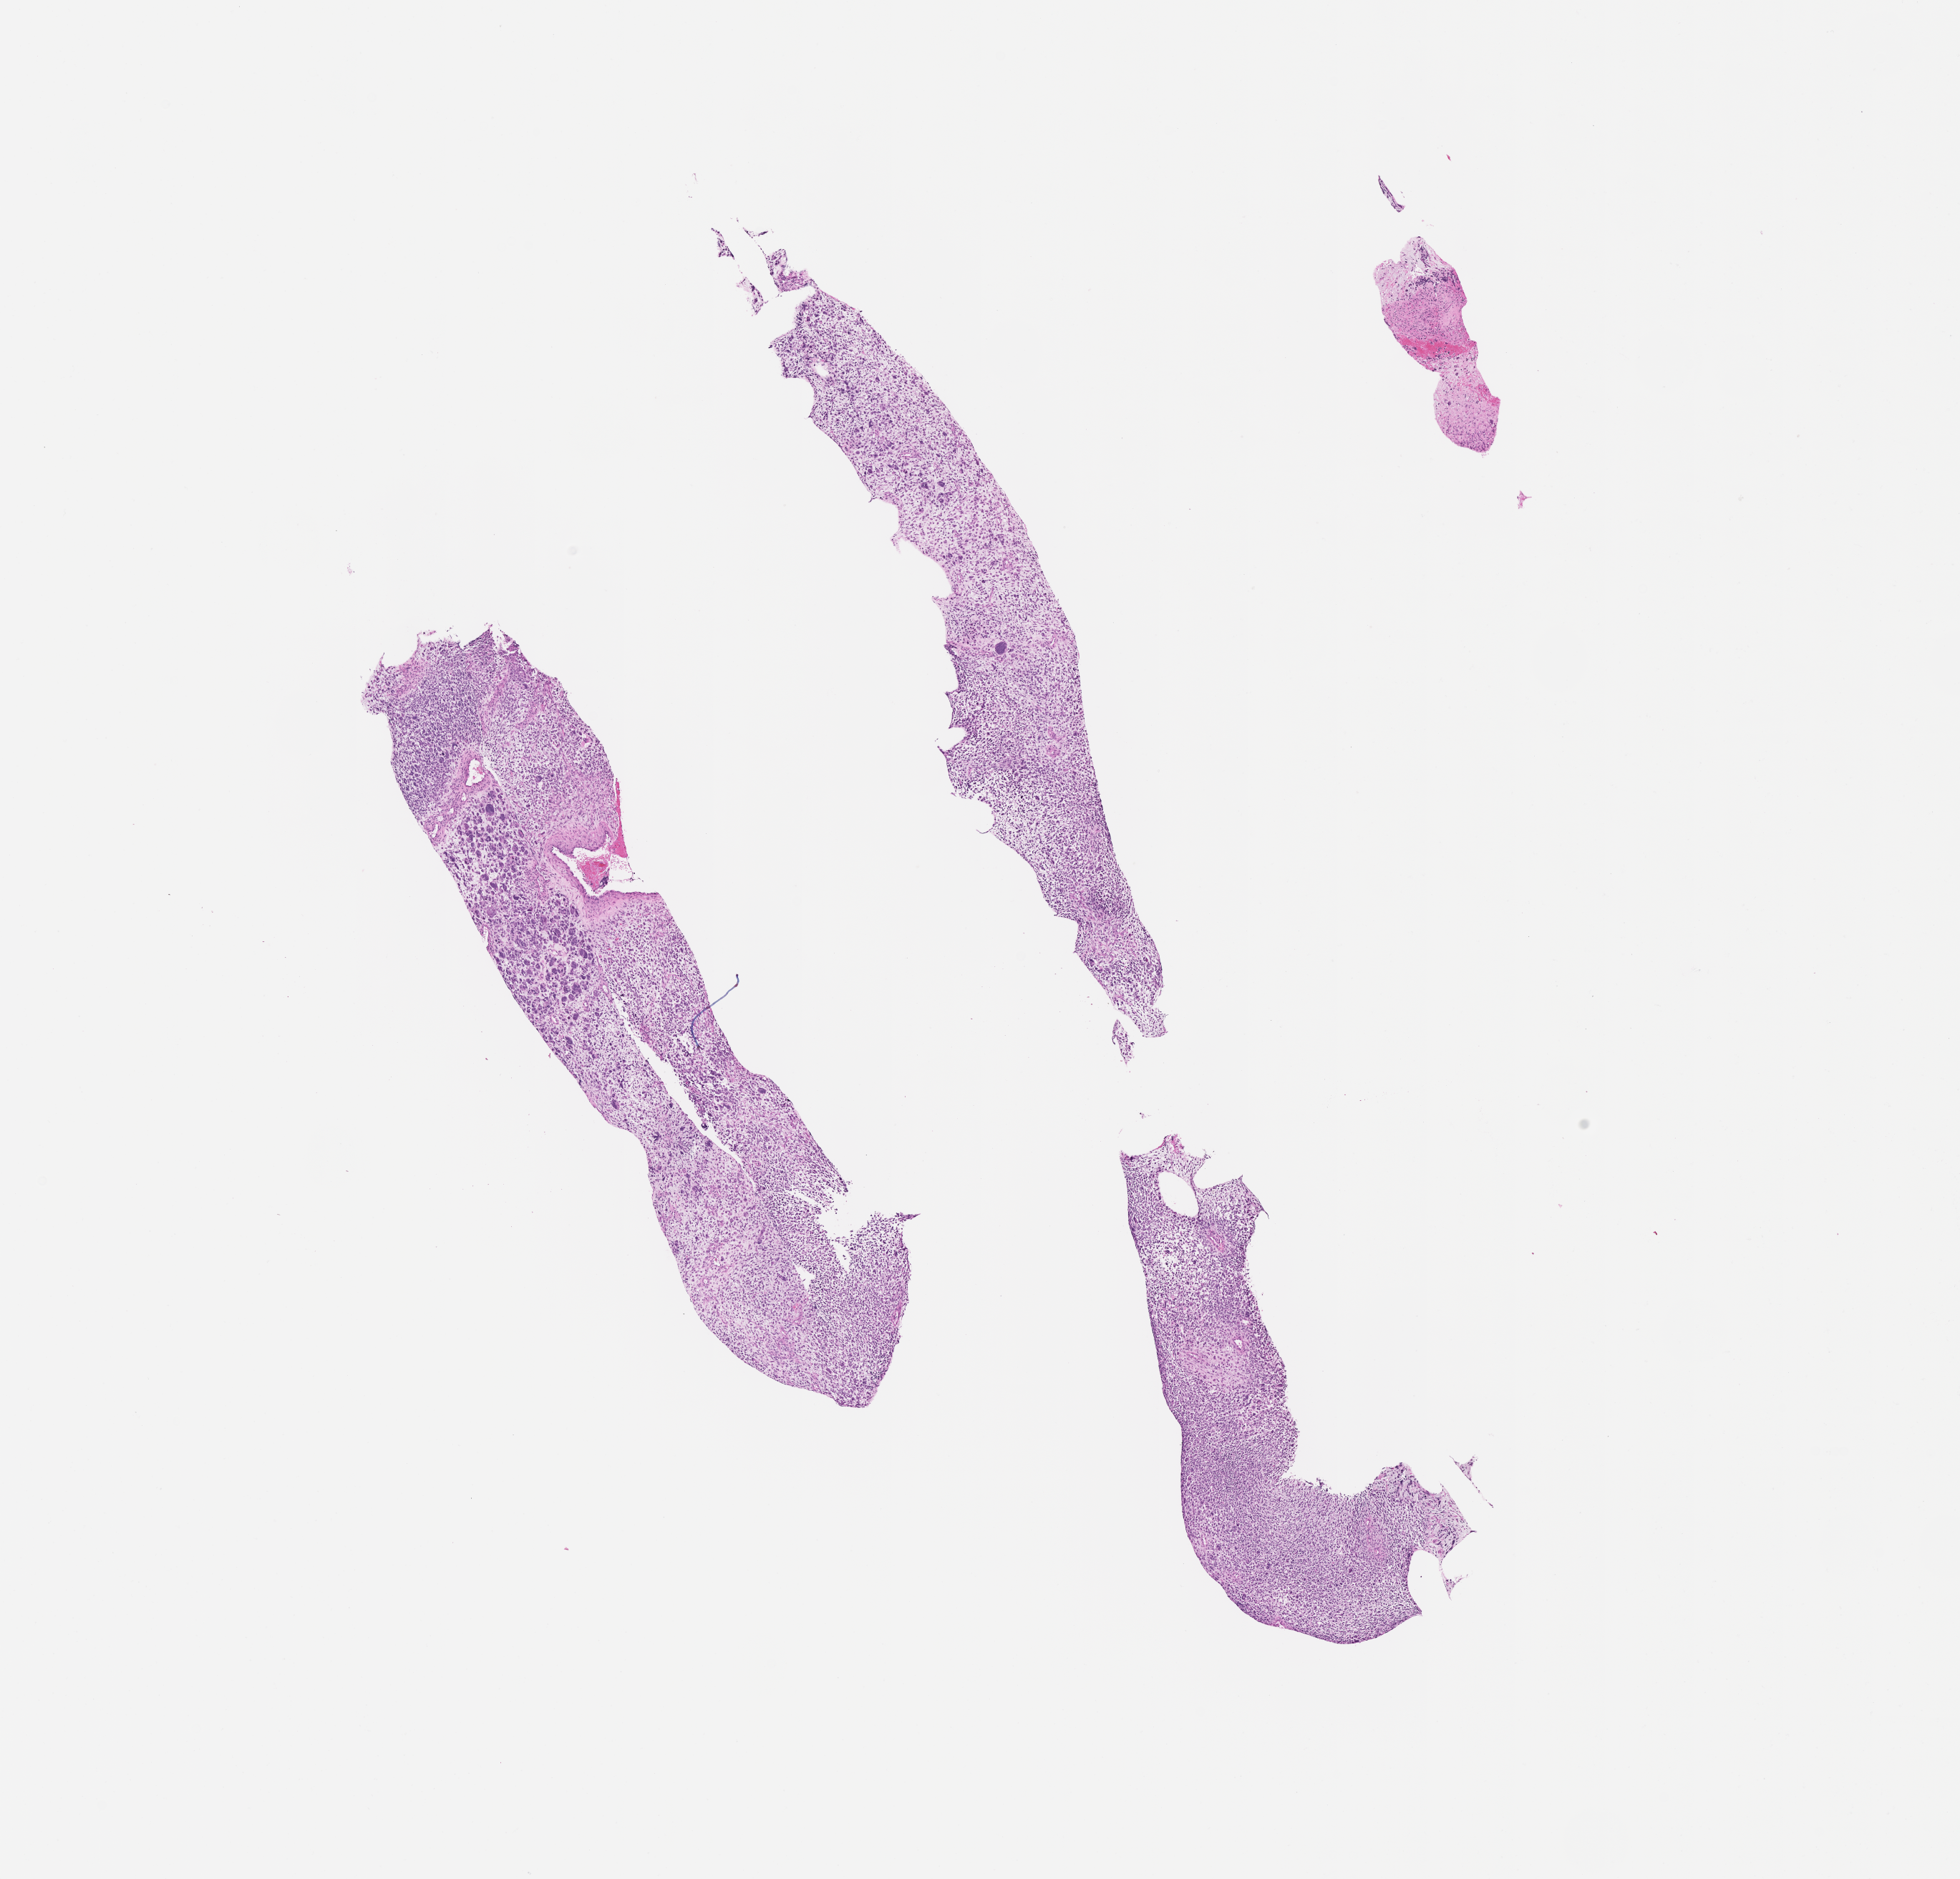
Hematoxylin and eosin (H&E) whole-slide image of tumor tissue, low-resolution overview of the scanned area, about 11.1 x 10.6 mm; FFPE section; site: pelvis. Patient: male, age 5.3 years at diagnosis.
- primary site (case record): bladder
- stage (as recorded): 3
- metastatic status at presentation (as recorded): non-metastatic (confirmed)
- diagnosis: rhabdomyosarcoma; histological classification: embryonal rhabdomyosarcoma